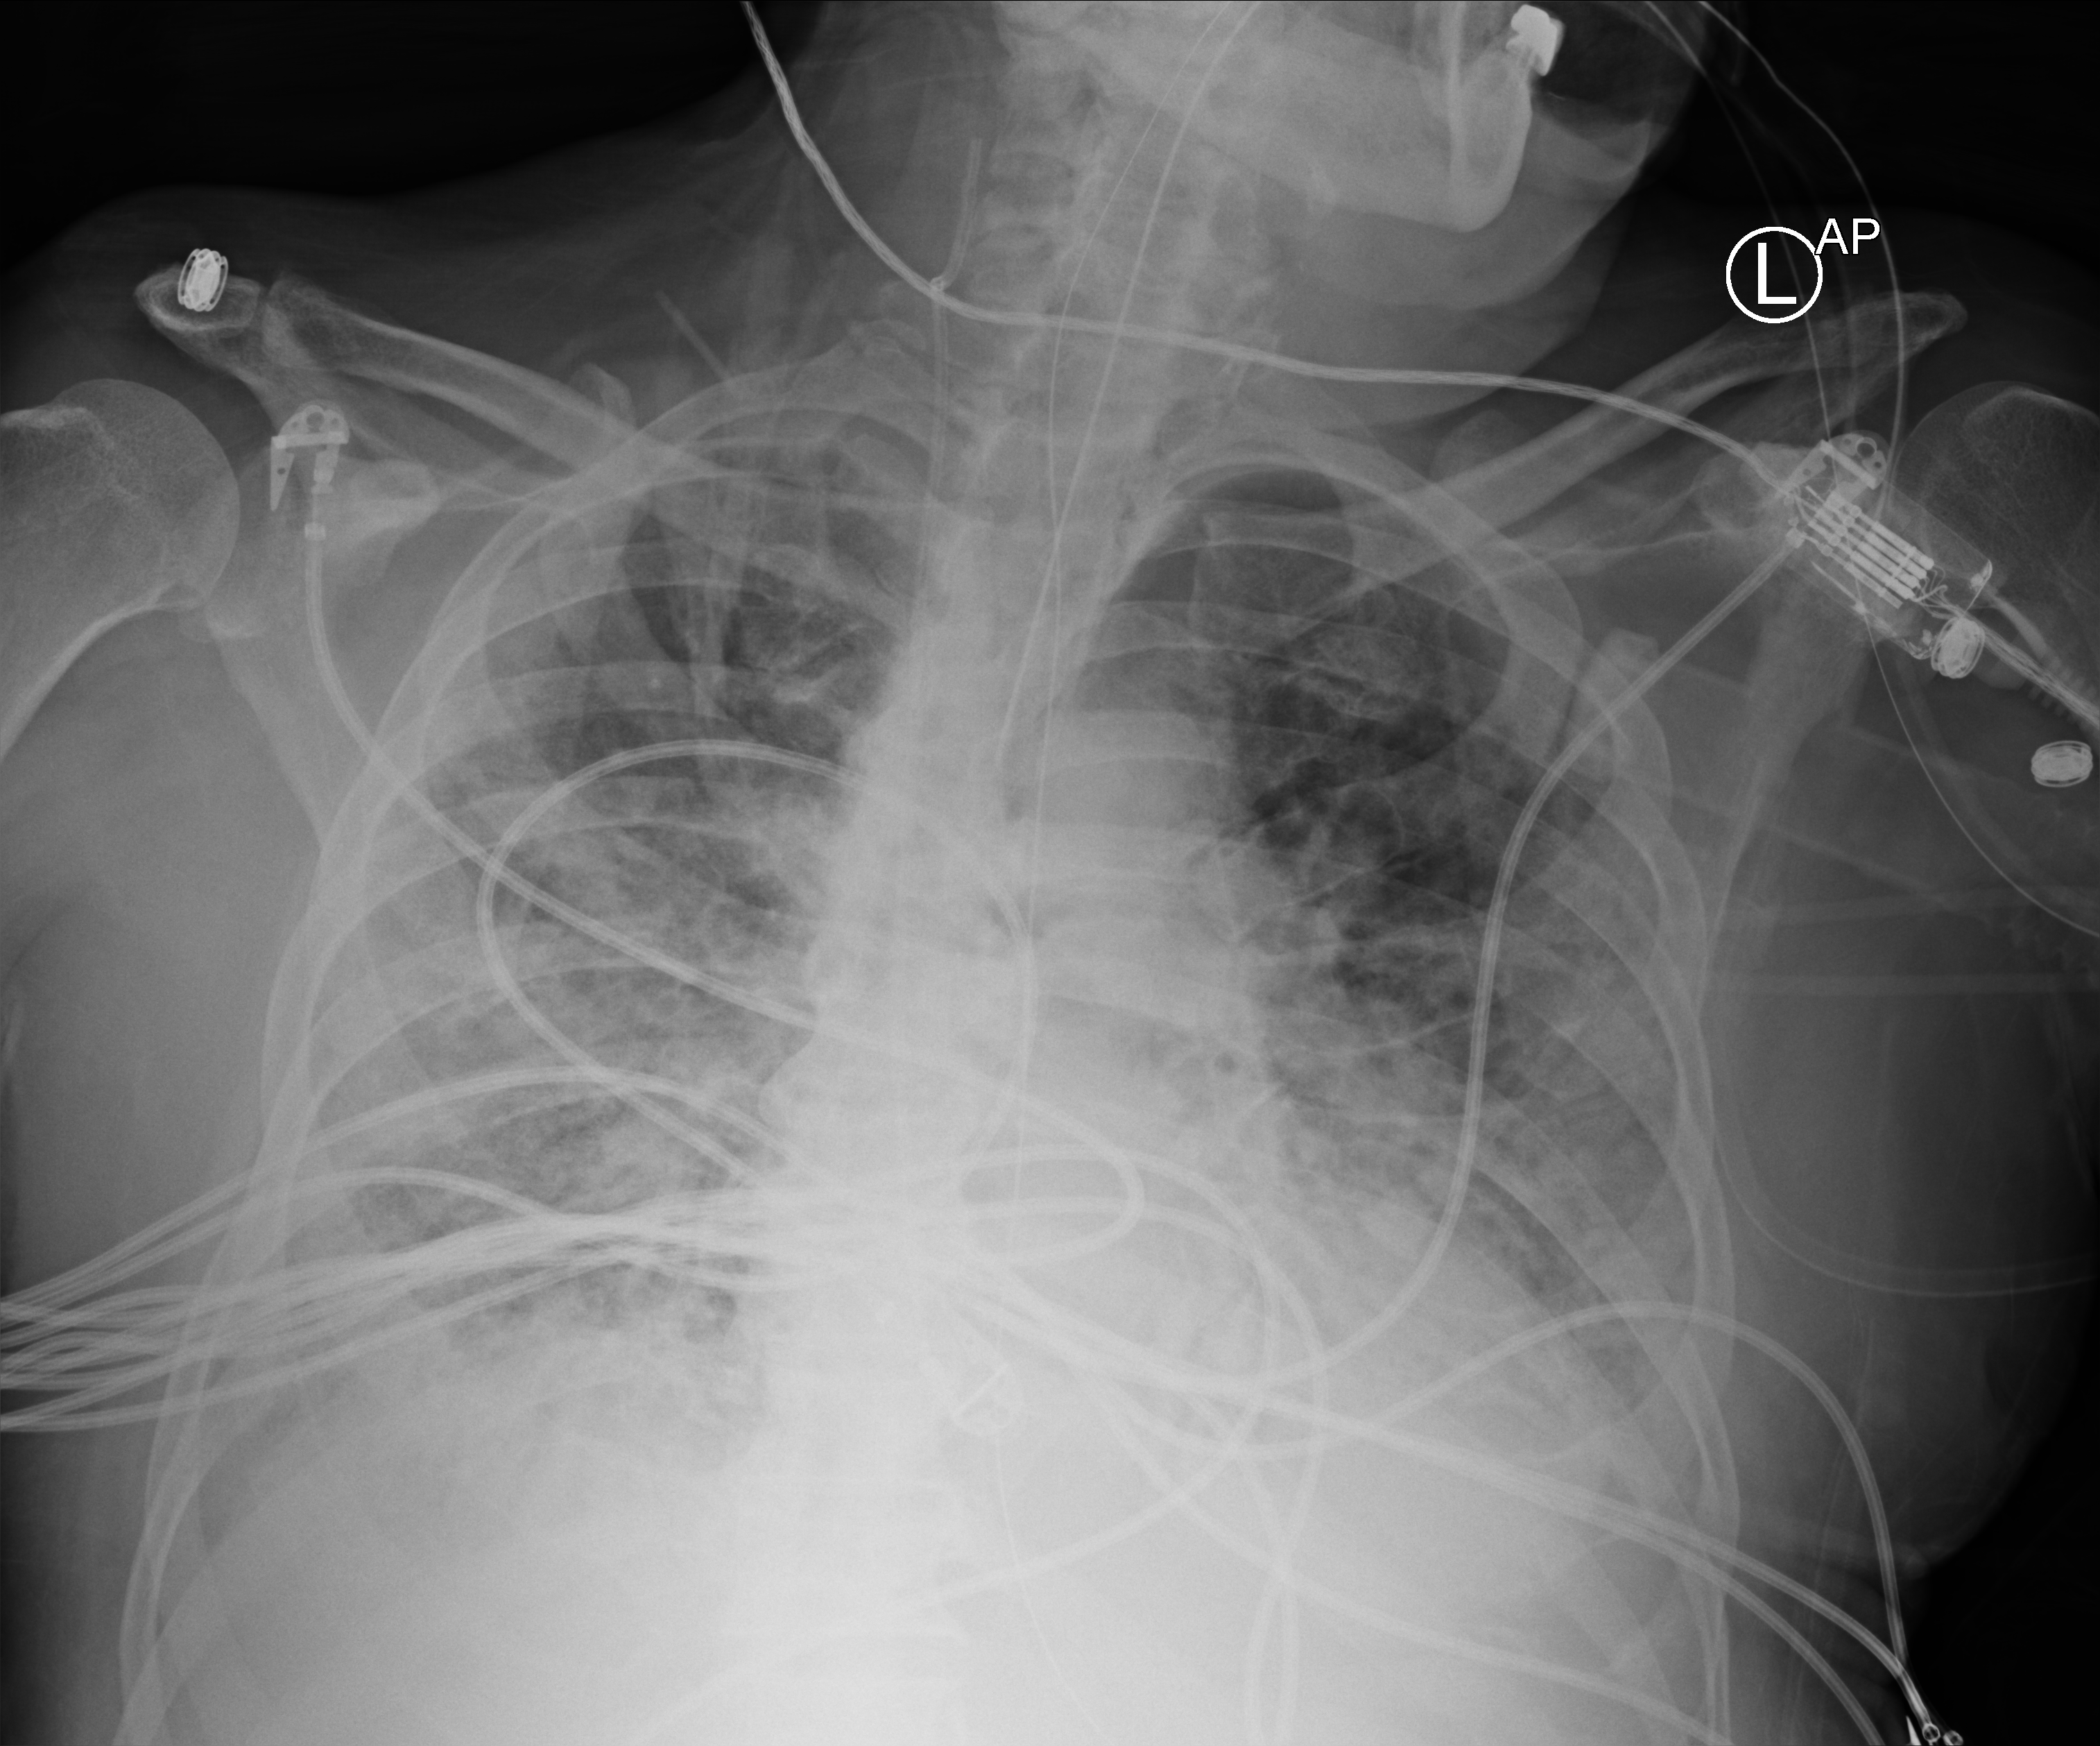
Portable chest radiograph; anteroposterior (AP) projection. Patient hospitalised with COVID-19; male, aged 75–90 years.
Admission-level facts for this patient (not findings on this image; timing relative to this image not recorded):
- admitted to intensive care during this hospital stay: yes